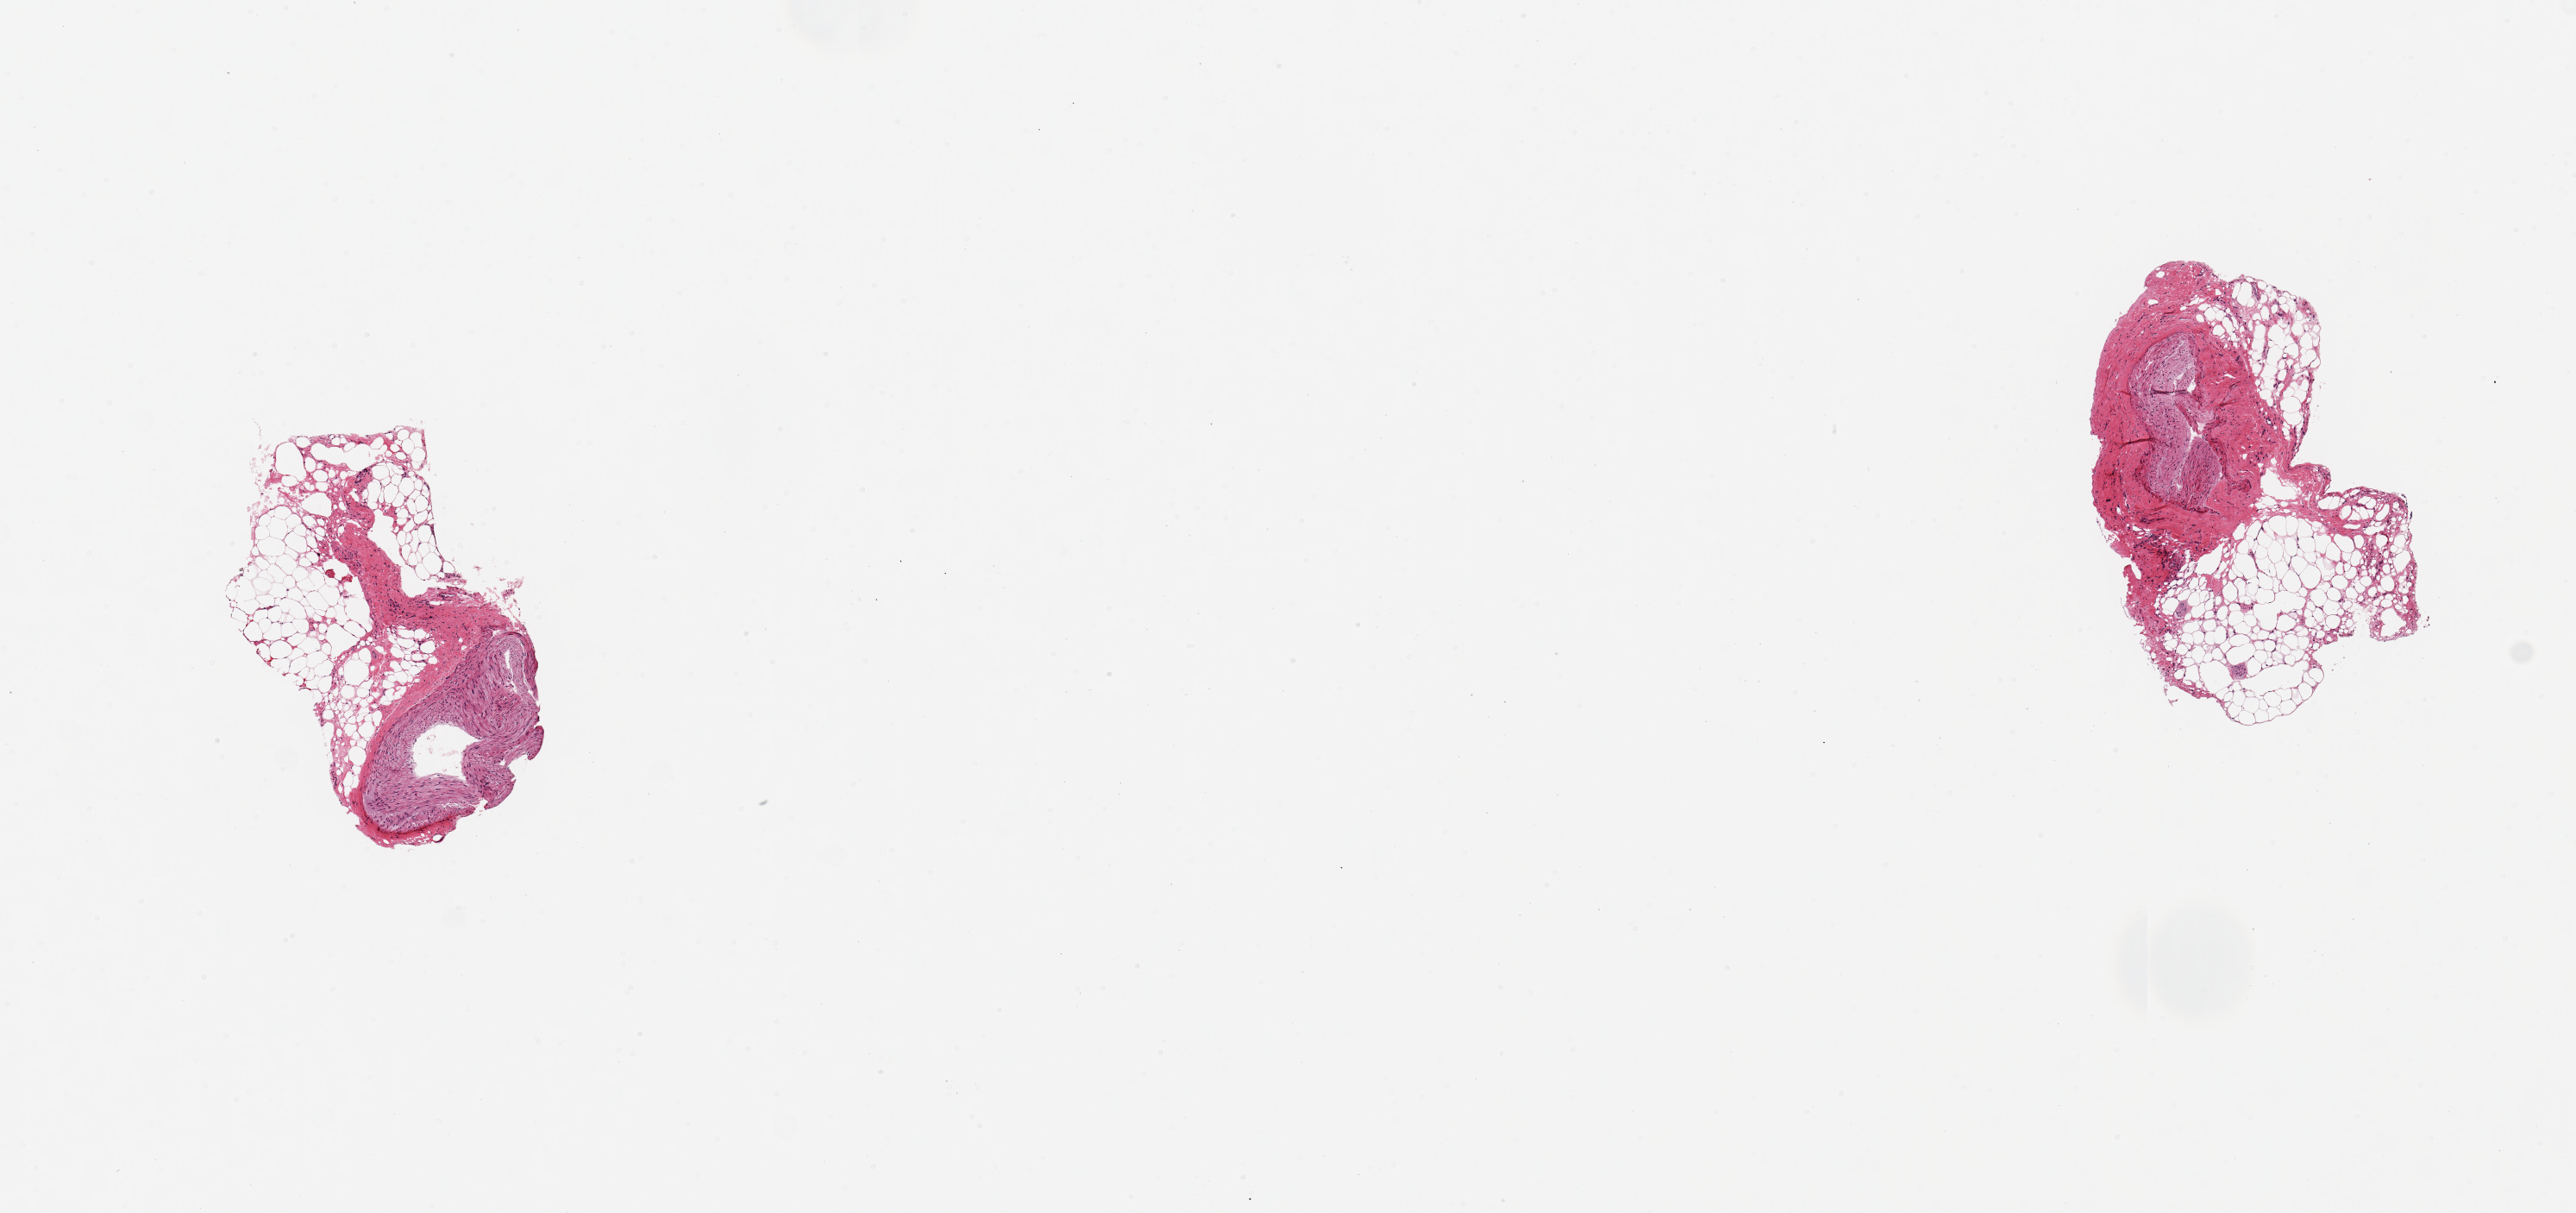
H&E whole-slide image, brightfield — whole scanned area (about 11.8 x 5.6 mm) shown as a low-resolution overview. PAXgene-fixed paraffin-embedded (PFPE) section. Sampled site (target tissue): coronary artery. Donor tissue sample. Donor: female.
- review note (as recorded): 2 pieces, 2x1 & 2x1mm; 60% extraneous adipose